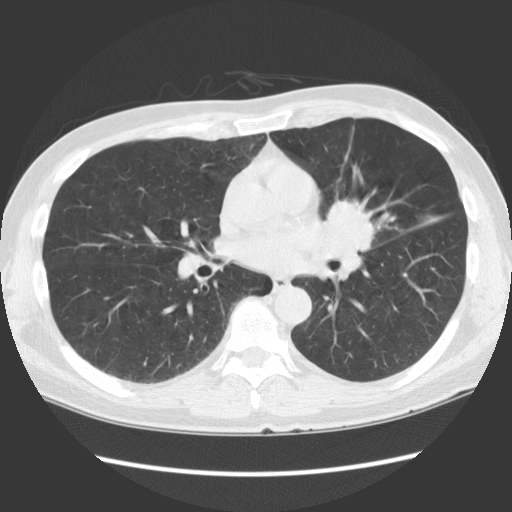
Low-dose screening chest CT, one axial slice. Slice 68 of 136 in the series (ordered by position). Reconstruction kernel STANDARD. 140 kVp. Lung window (W 1500 / L -600 HU). 2.5 mm slice thickness. 512 × 512 image matrix, field of view 360 × 360 mm.
Structures marked on this image (manually delineated by an expert):
- lesion 1 (tumor, hilum of left lung): box from (x=322, y=199) to (x=376, y=253) px